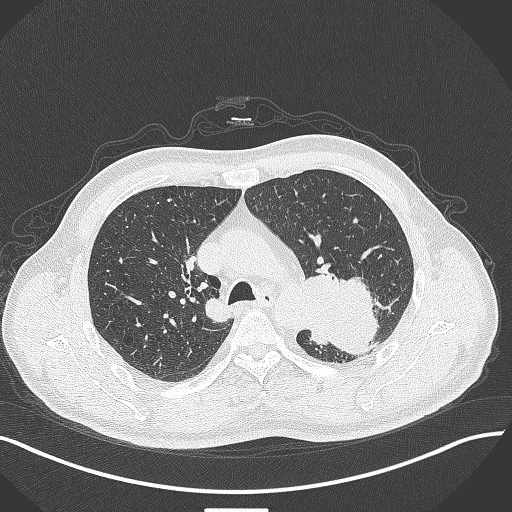
Chest CT, one axial slice. Position 295 of 429 along the scan axis. Reconstruction kernel B70f. Lung window (W 1500 / L -600 HU). 1 mm slice thickness. 512 × 512 image matrix. Patient: male, 55 years. Case-level facts recorded for this patient, not image findings: clinical TNM (as recorded): T3 N0 M1c; histopathological grade: G3.
Outlined on this slice (bounding box drawn by a radiologist):
- lung tumour (recorded histology: adenocarcinoma): box from (x=294, y=261) to (x=384, y=355) px